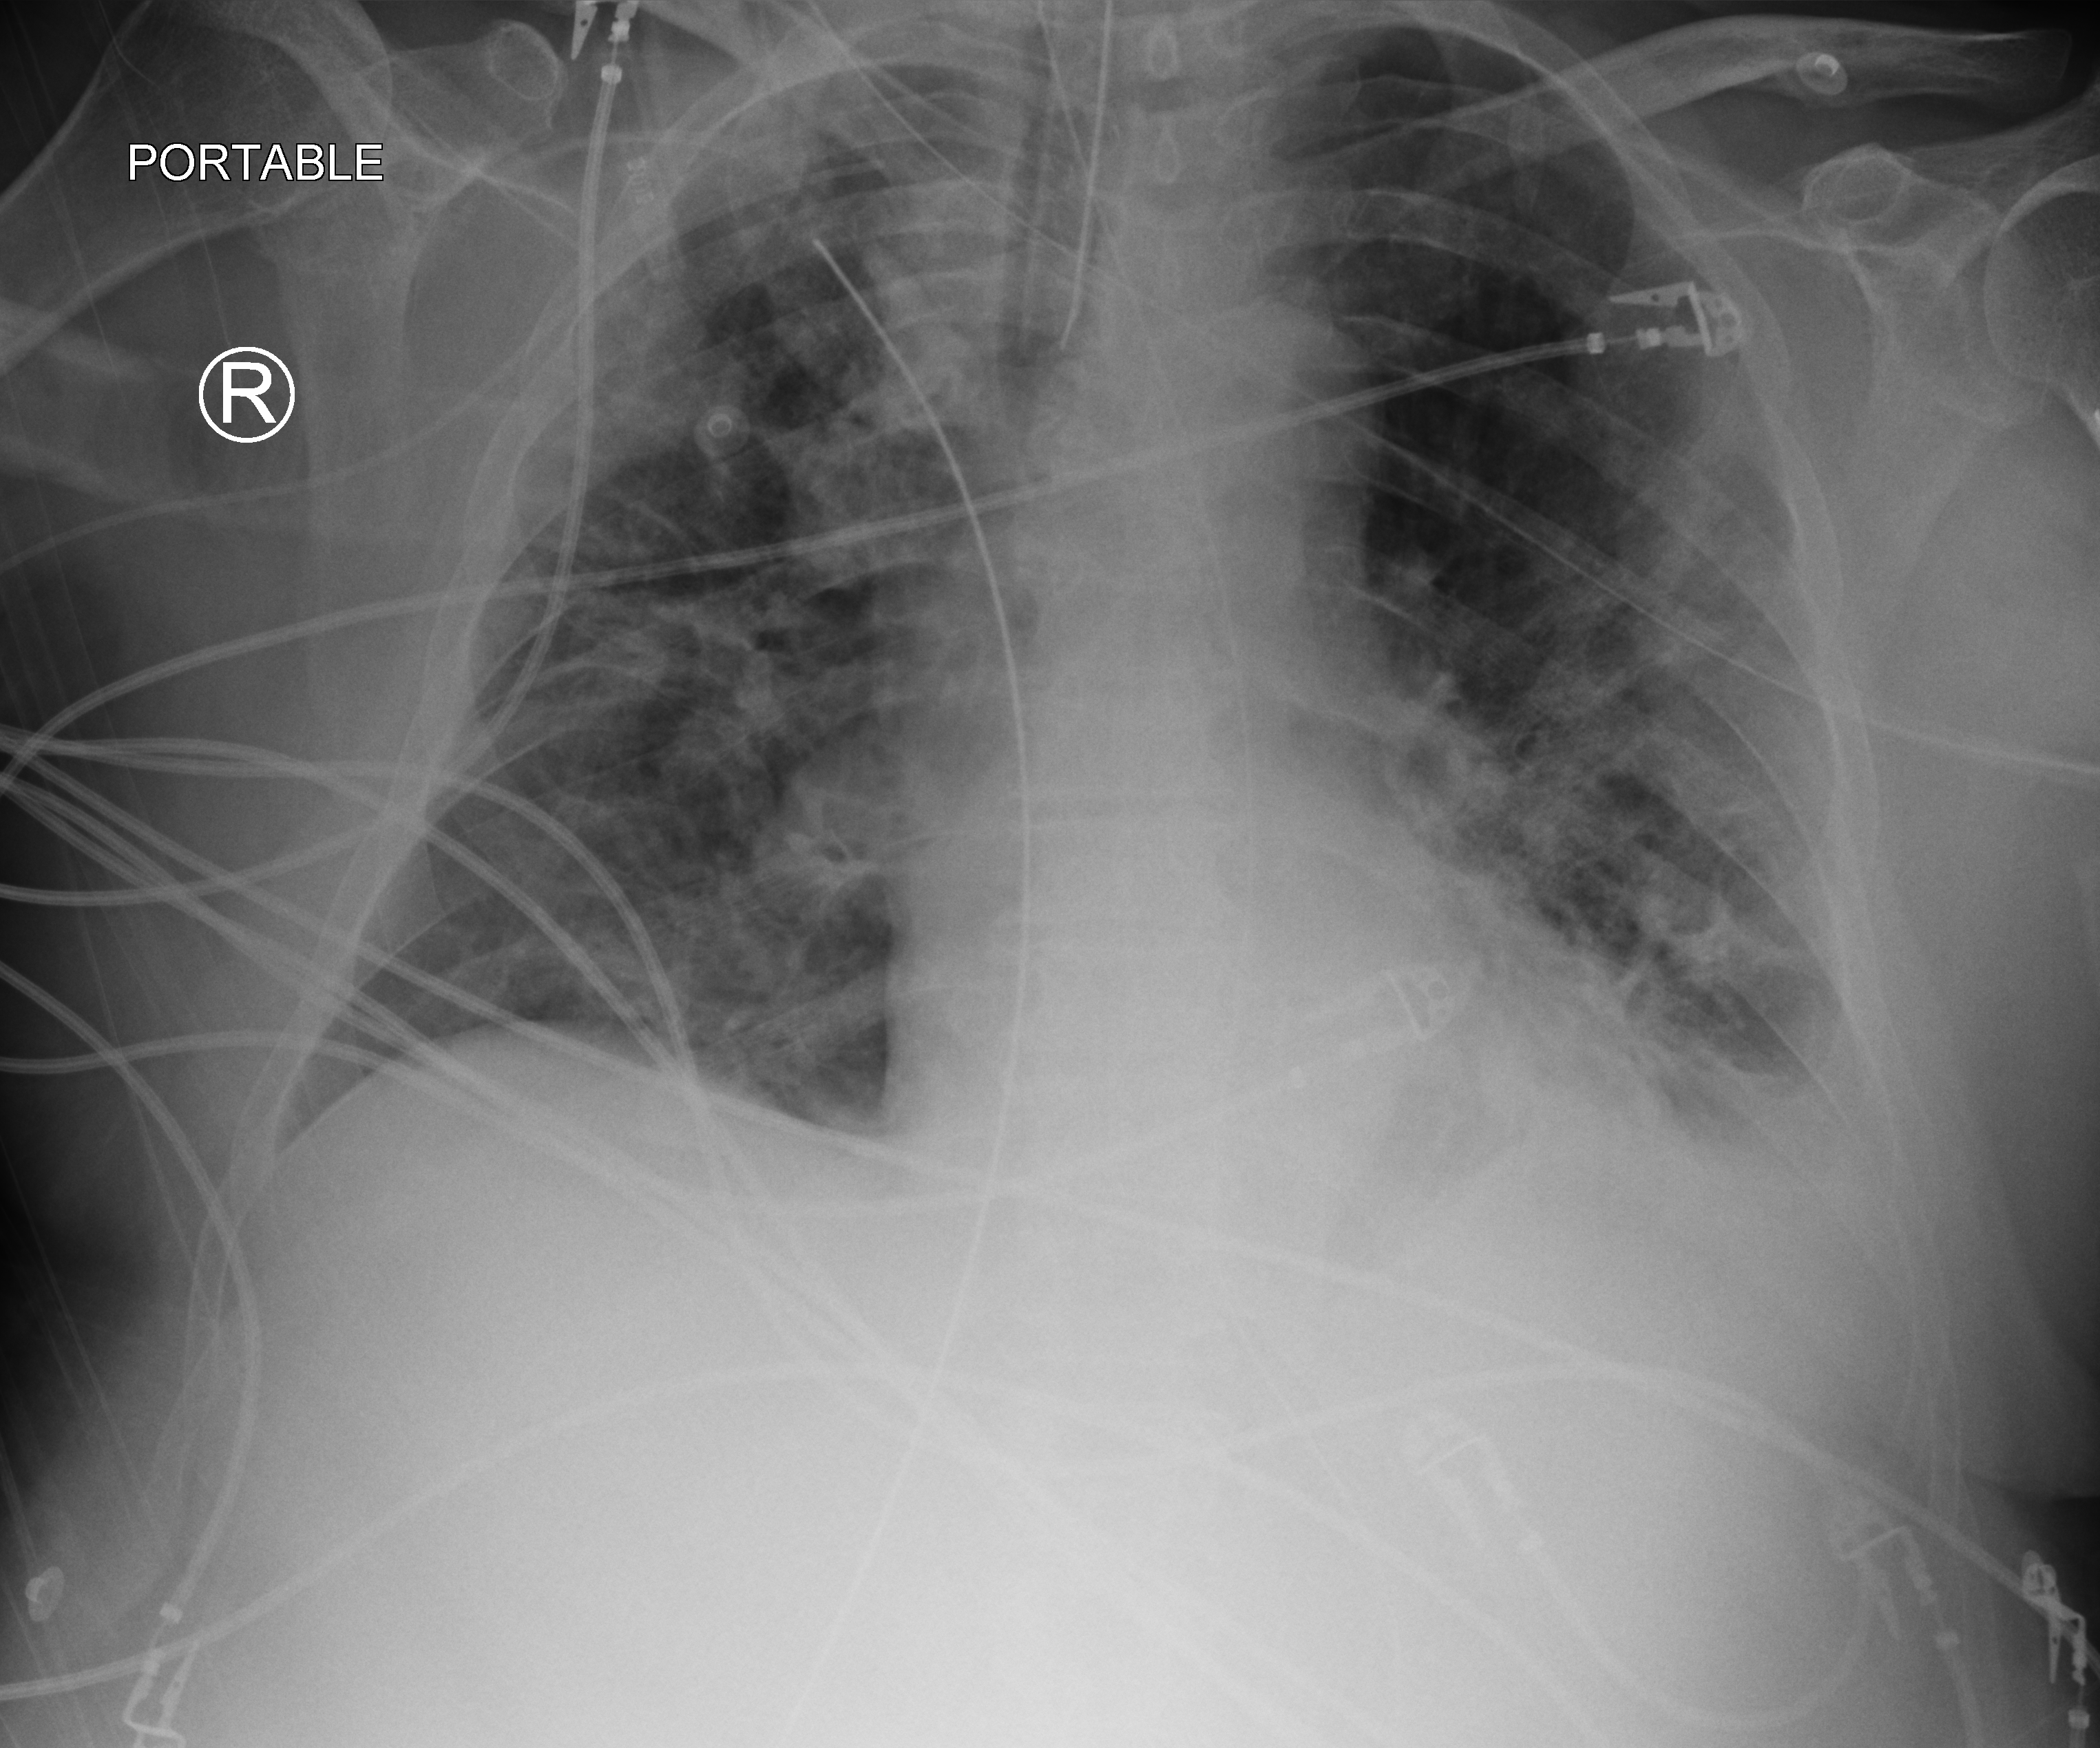
Chest X-ray (portable); anteroposterior (AP) projection. Patient hospitalised with COVID-19; male, aged 60–74 years.
Hospital-stay facts (about this admission, not read from this image; timing relative to this image not recorded): admitted to intensive care during this hospital stay: yes; diabetes (admission record): no.